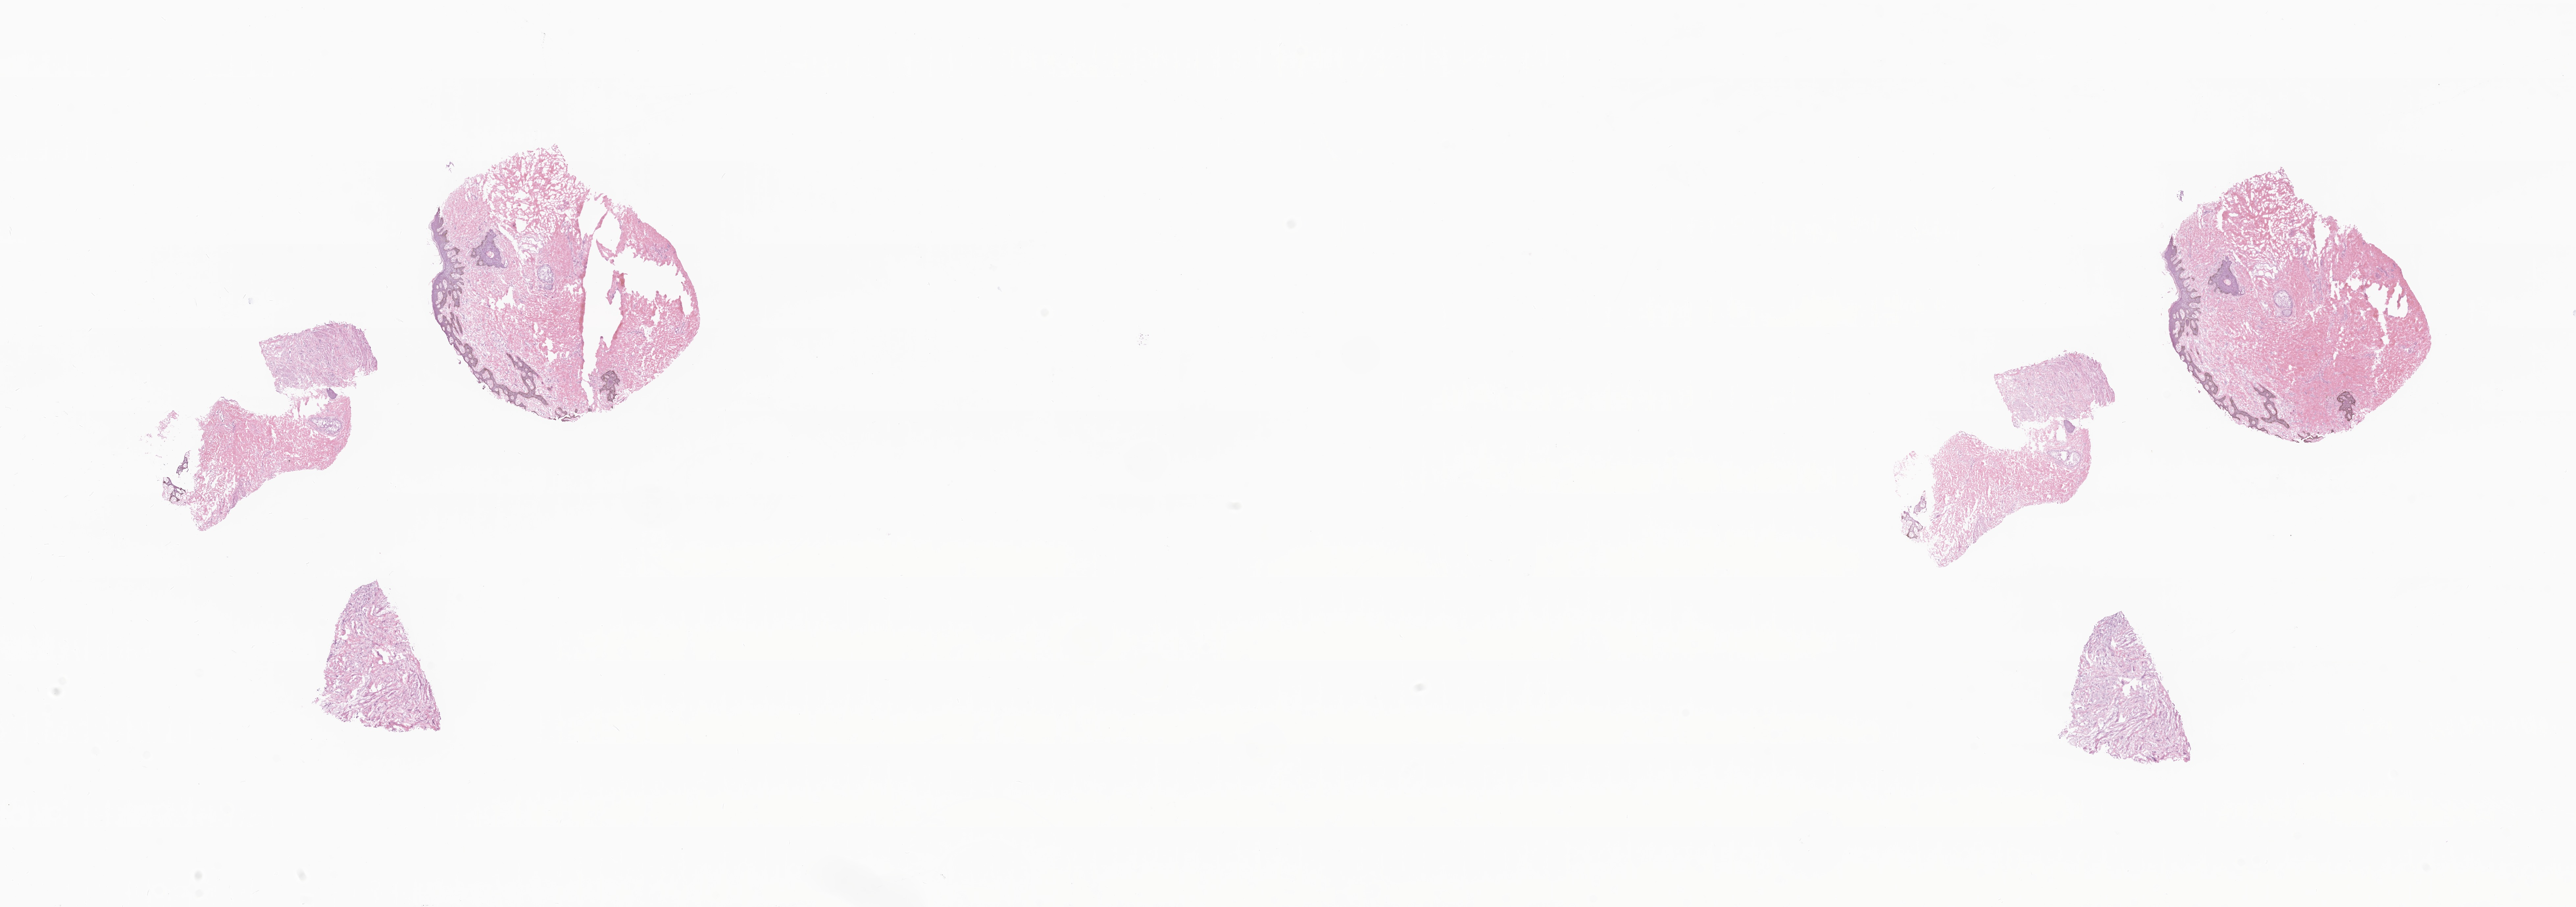
Digitized haematoxylin and eosin-stained section, a low-resolution overview of the entire scanned area, about 33.0 x 11.6 mm, cryosection, specimen: primary tumor, site: breast. Patient: female, age at initial diagnosis 64 years. Pathologist review of this section (percent, as recorded): tumor cells 6%, tumor nuclei 50%, stromal cells 88%, necrosis 0%, normal cells 6%. Inflammatory infiltration, as recorded: lymphocyte infiltration 18%, monocyte infiltration 0%, neutrophil infiltration 0%.
• diagnosis: Metaplastic carcinoma, NOS